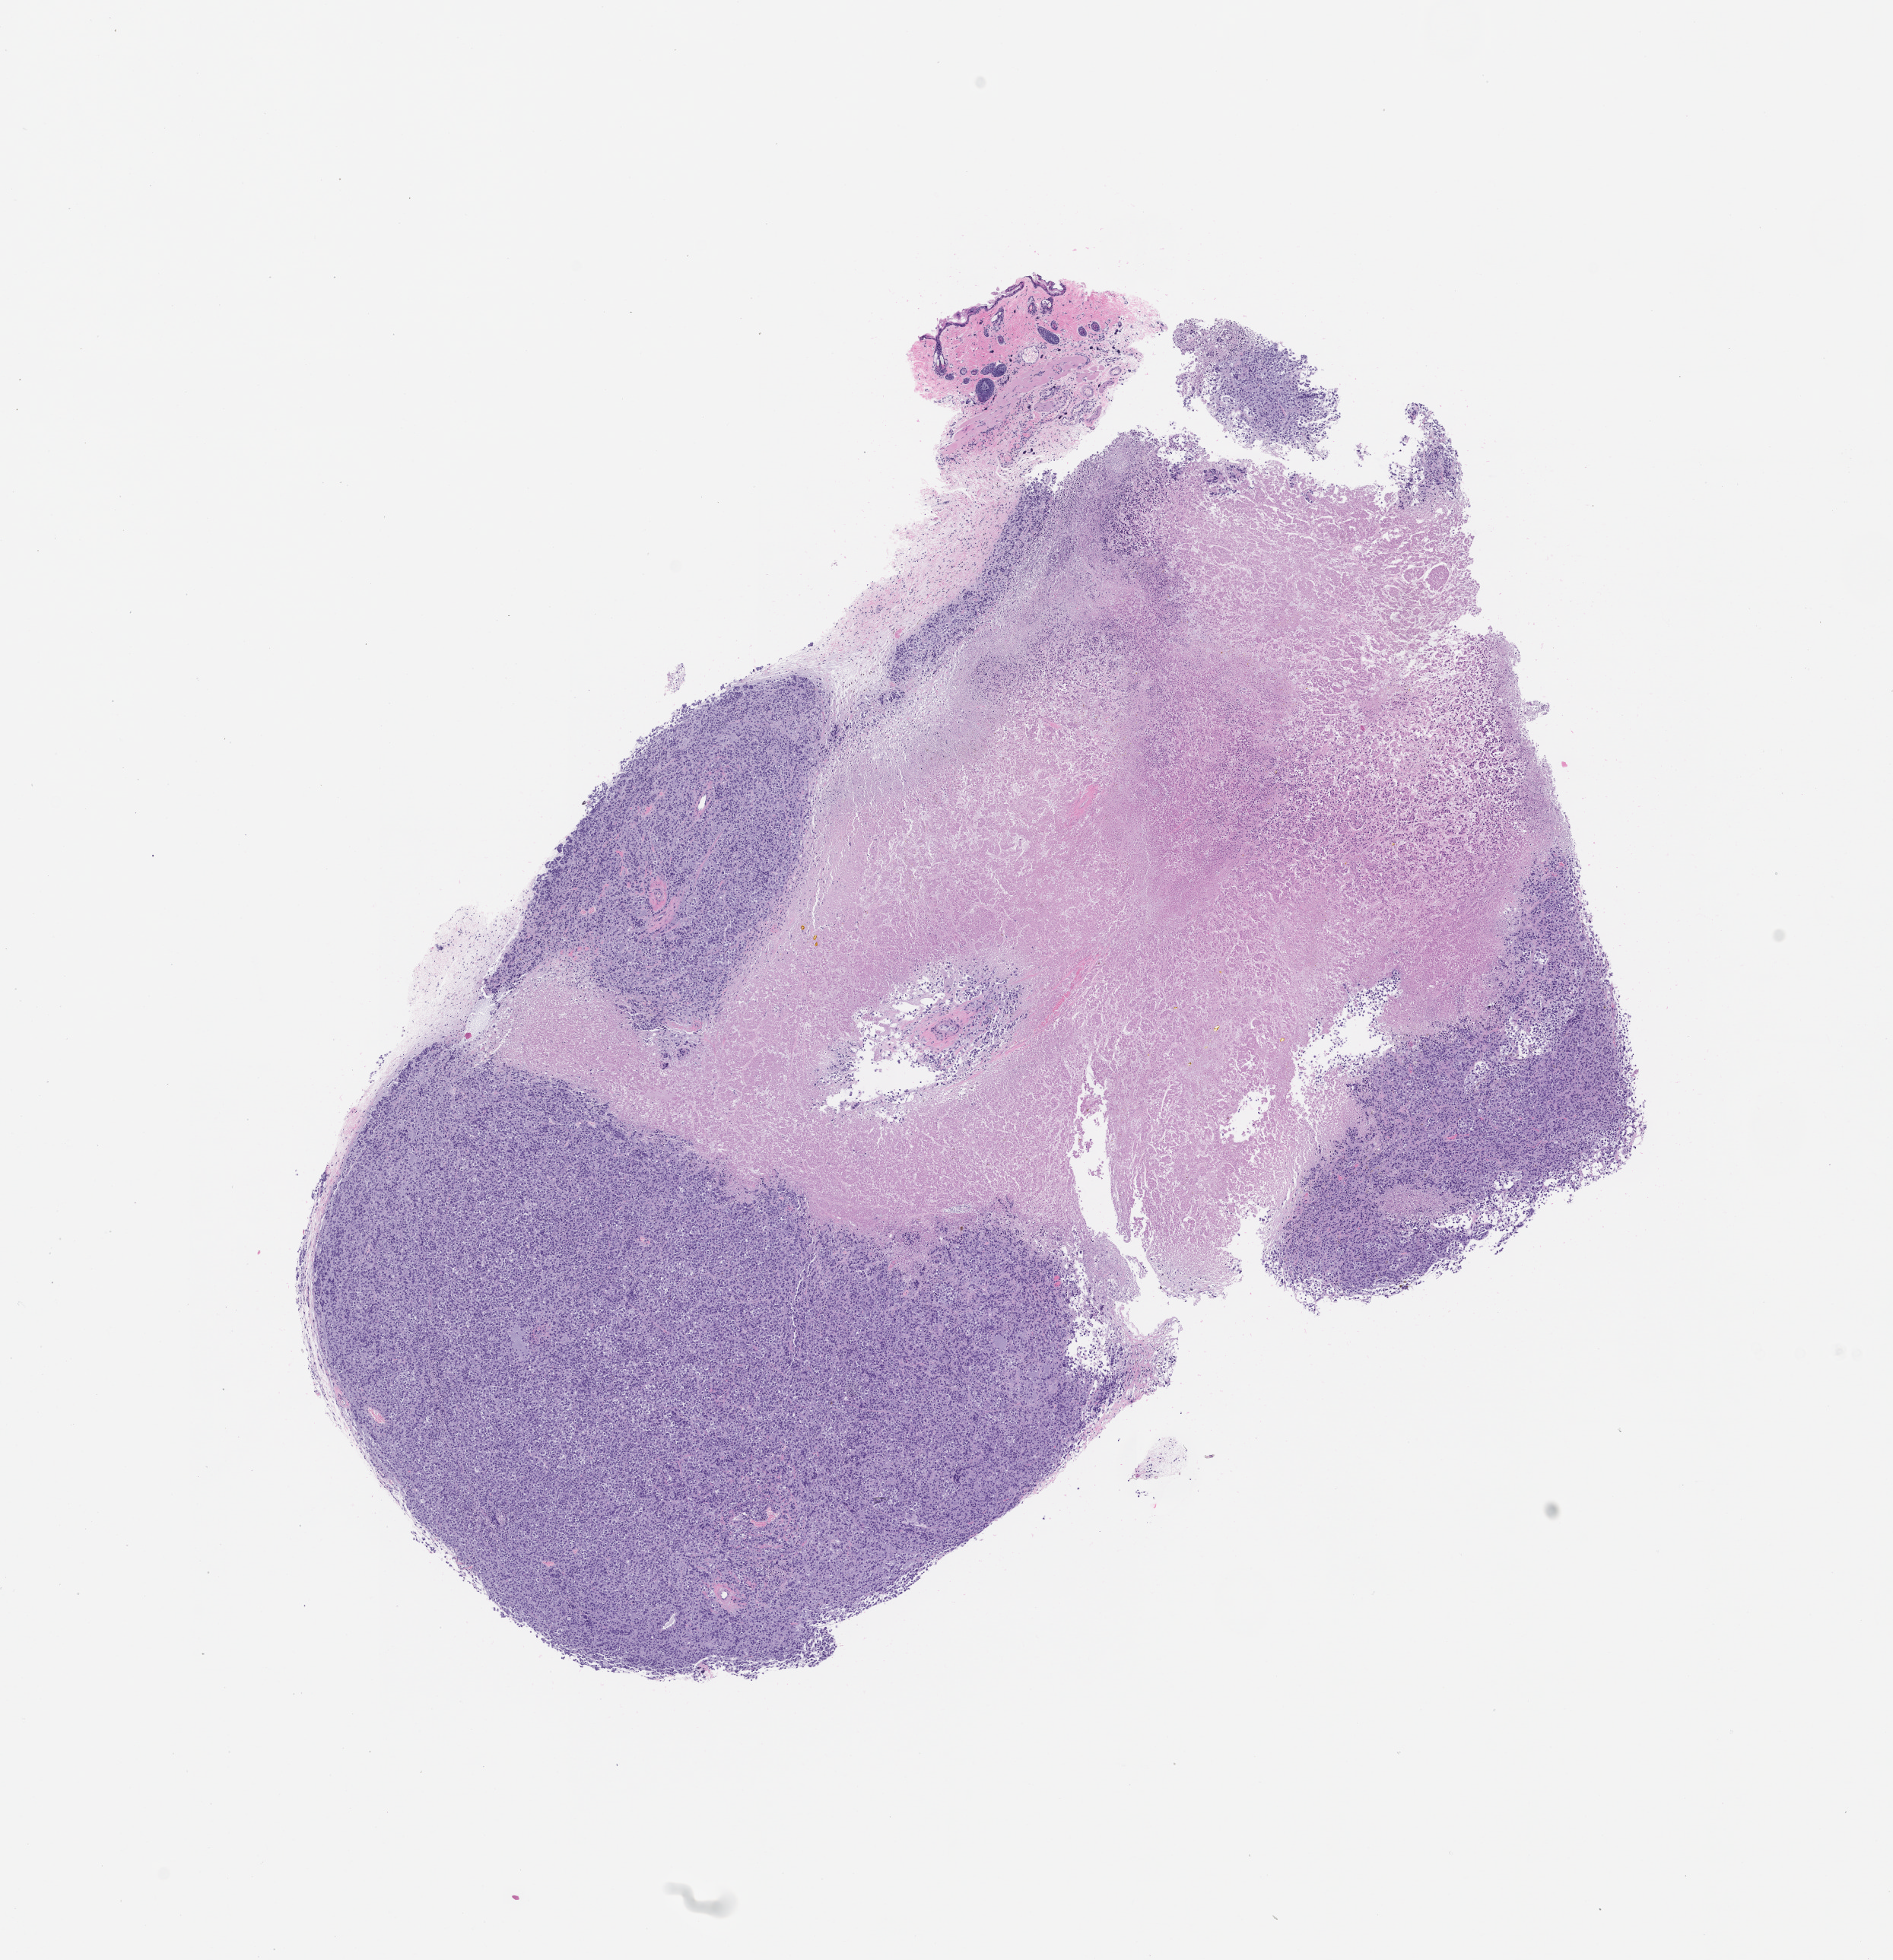
Whole-slide image, haematoxylin and eosin: patient-derived xenograft (human tumor grown in a mouse), passage 0, low-resolution overview of the scanned area, about 10.0 x 10.3 mm, formalin-fixed paraffin-embedded section, originating tumor site category: skin.
- originating patient diagnosis: Melanoma